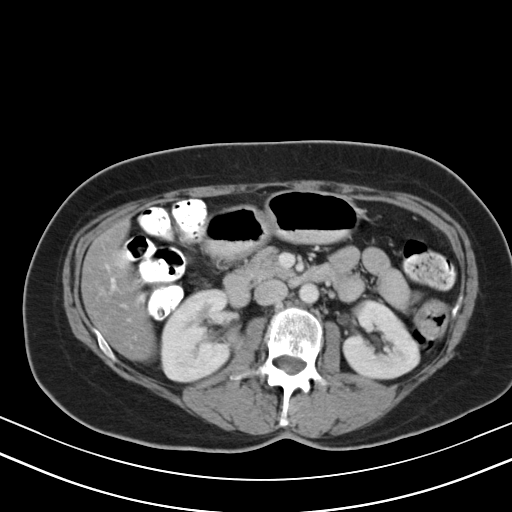
Contrast-enhanced abdominal CT, one axial slice. Position 20 of 47 along the scan axis. Reconstruction kernel B40s. Soft-tissue window (W 400 / L 40 HU). 512 × 512 image matrix. Female patient. Case-level facts recorded for this patient, not image findings: diagnosis: colorectal cancer liver metastases, imaged before liver resection; multiple liver metastases: no; largest metastasis: 3.5 cm; disease in both lobes: no.
Outlined on this slice (outlined manually by an expert reader):
- hepatic veins: bounding box [x1, y1, x2, y2] px = [110, 278, 115, 287]
- liver: [83, 225, 154, 359]
- planned liver remnant (the part of the liver to remain after resection): [84, 225, 154, 359]
- portal vein (with intrahepatic branches): [138, 278, 142, 281]